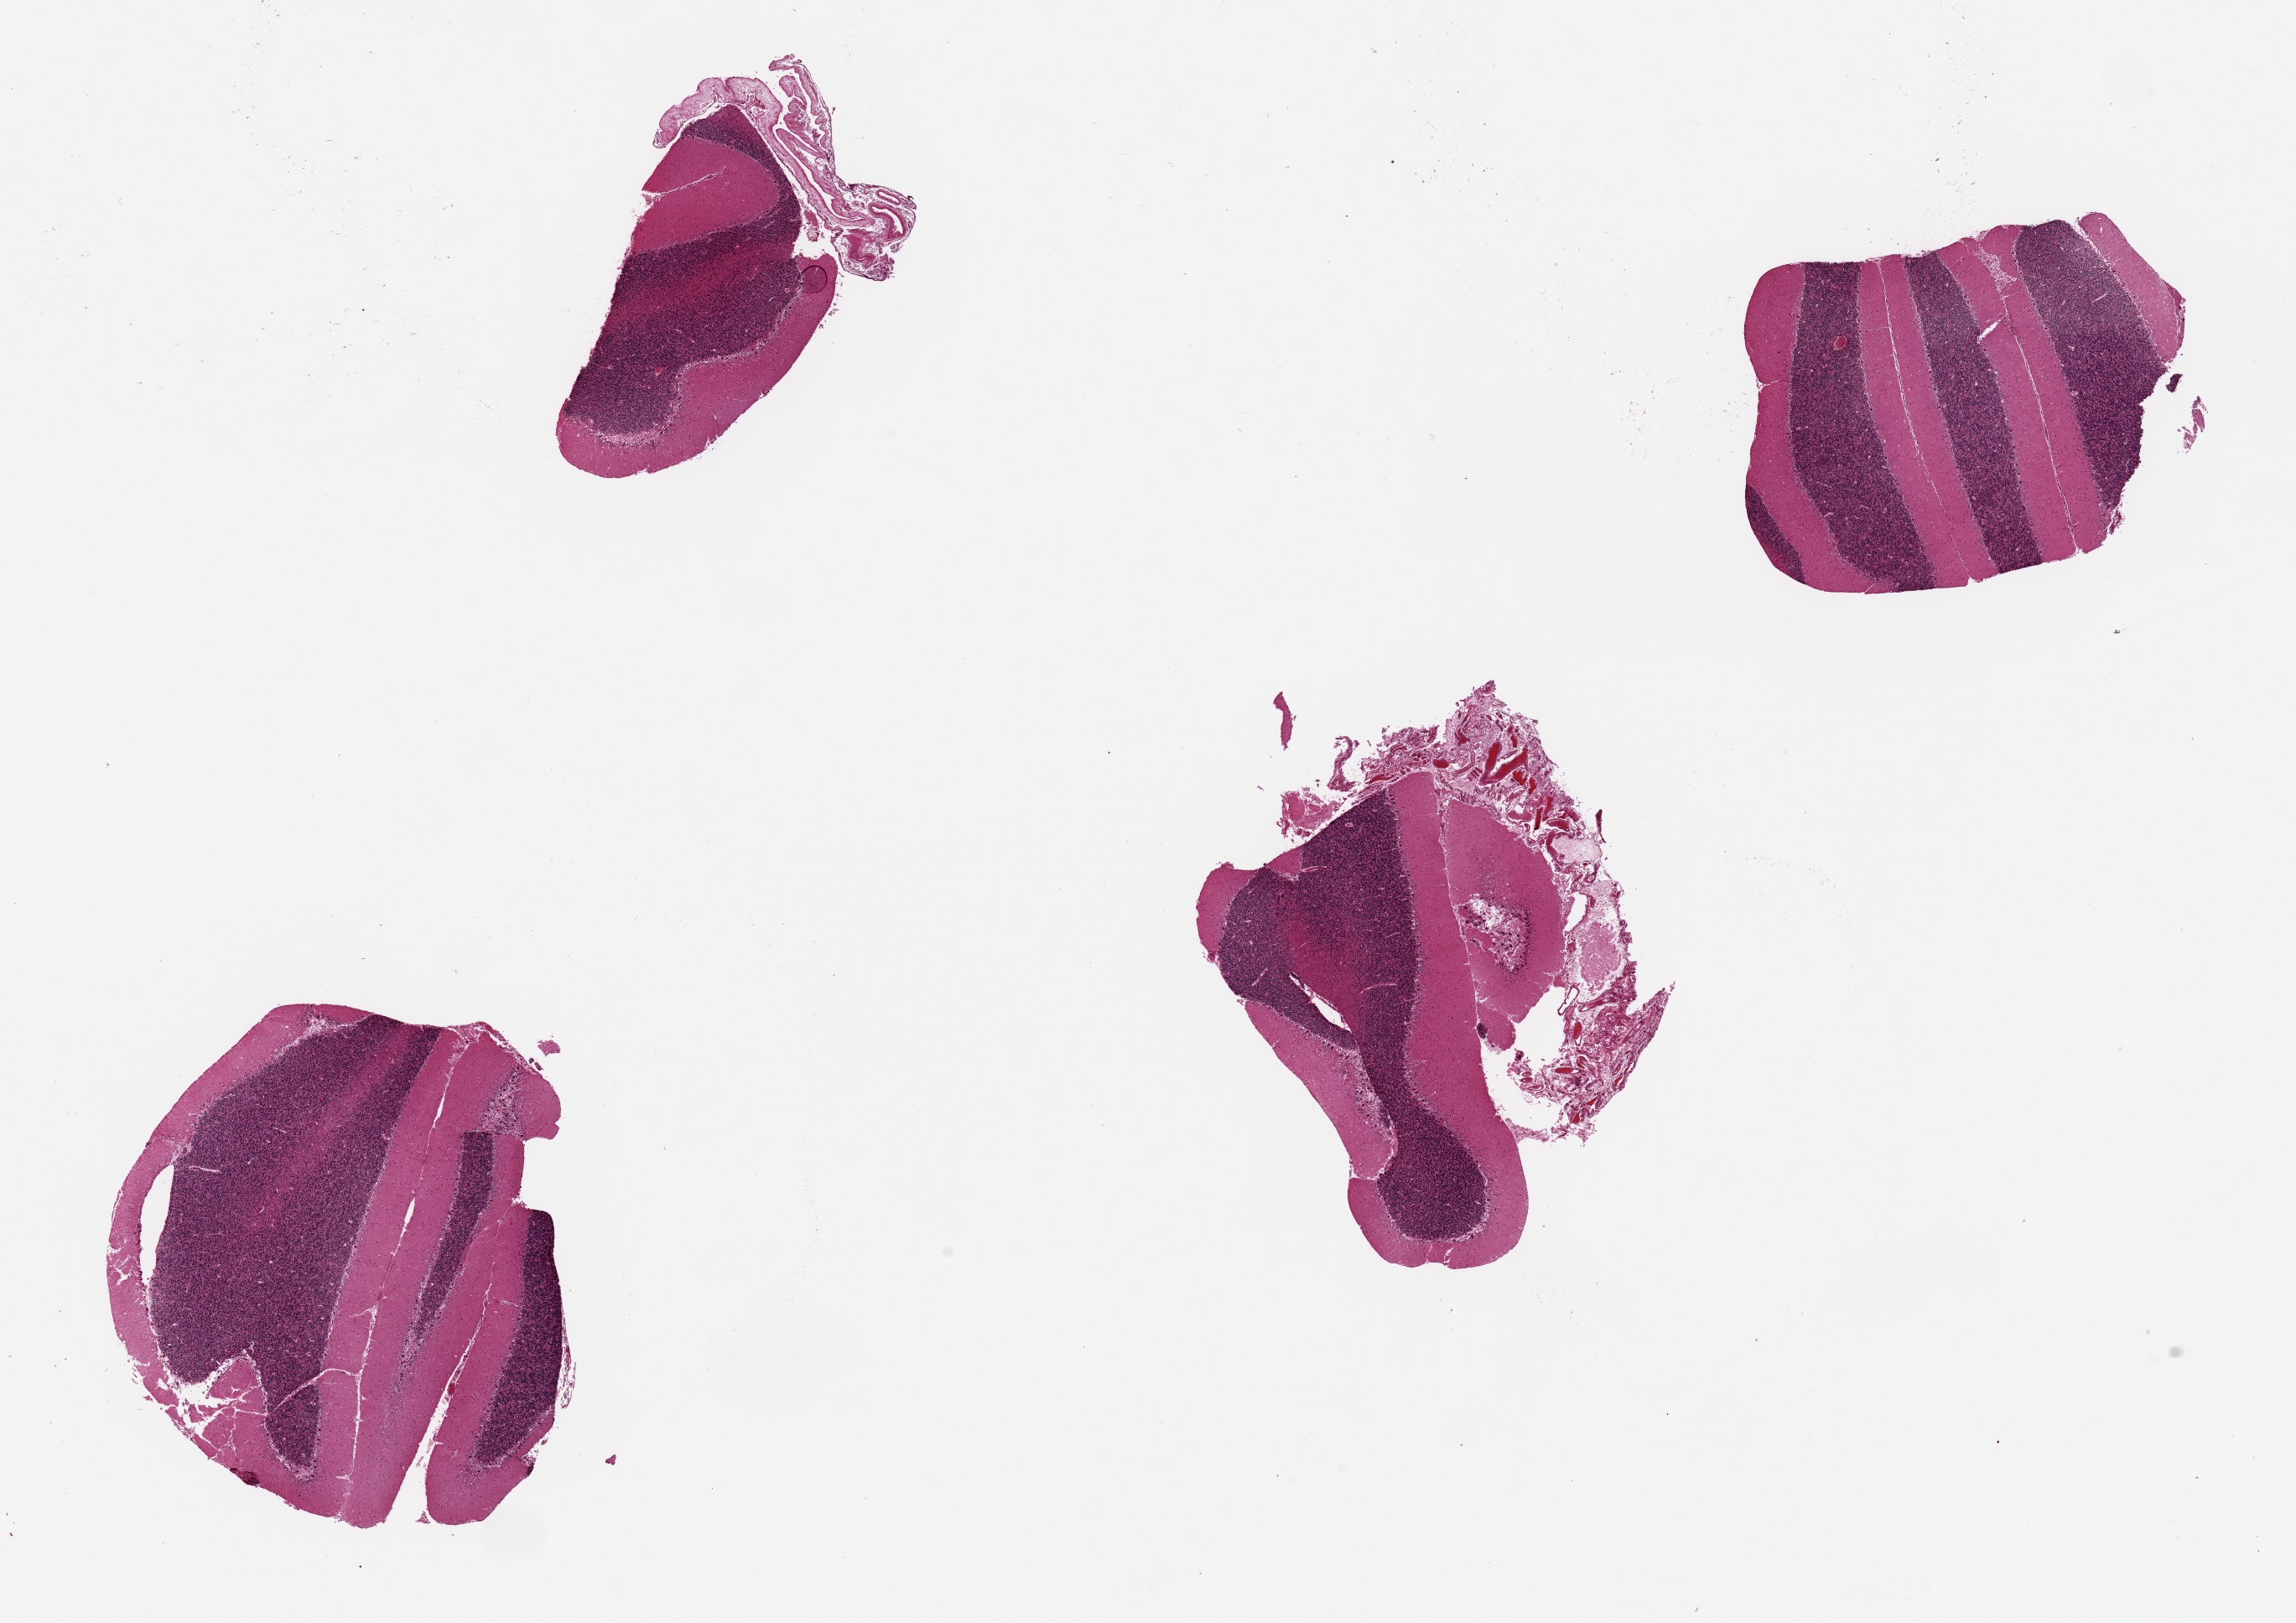
Digitized H&E-stained section, brightfield, shown as a low-resolution overview of the whole scanned area (about 21.7 x 15.3 mm), PAXgene-fixed, paraffin-embedded tissue, target tissue: cerebellum, tissue donor sample. Male donor.
Review note (as recorded): 4 pieces, ~4x3mm.